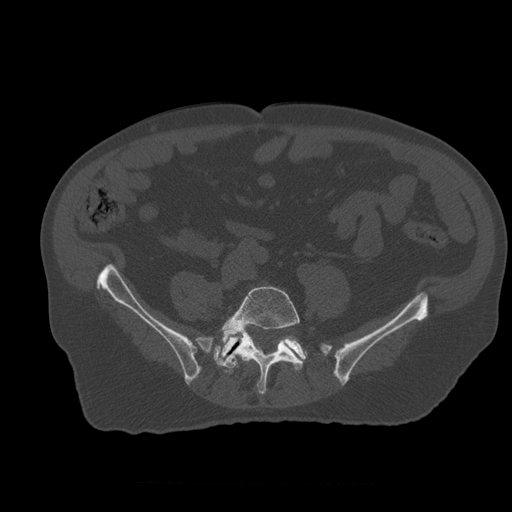
CT including the spine, one axial slice. Position 140 of 399 along the scan axis. Reconstruction kernel STANDARD. 120 kVp. Bone window (W 1800 / L 400 HU). 1.25 mm slice thickness. 512 × 512 image matrix, field of view 407 × 407 mm. Patient age 73 years. From the clinical record (not read from this slice): primary cancer: prostate; vertebrae with lytic lesions (as recorded): L2.
Structures marked on this image (semi-automatically segmented with operator editing):
- L4 vertebra: bounding box <242,353,251,361> (left, top, right, bottom; pixels)
- L5 vertebra: <214,286,303,395>